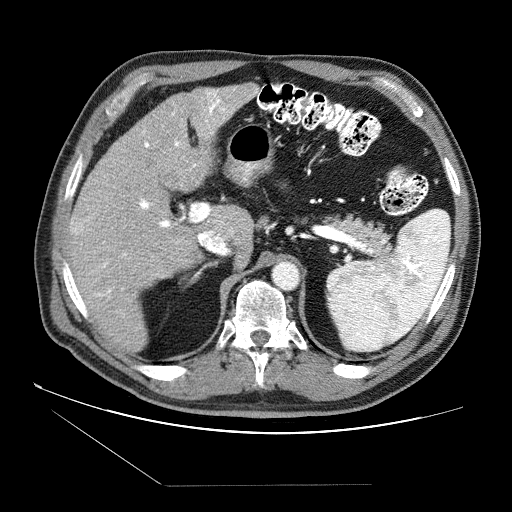
Contrast-enhanced abdominal CT (liver protocol), one axial slice; position 49 of 87 along the scan axis; reconstruction kernel STANDARD; 120 kVp; soft-tissue window (W 400 / L 40 HU); 2.5 mm slice thickness; 512 × 512 image matrix, field of view 400 × 400 mm. From the clinical record (not read from this slice): diagnosis: hepatocellular carcinoma (patient treated with transarterial chemoembolisation; whether this scan precedes or follows treatment is not stated here); TNM stage (as recorded): Stage-II; Child-Pugh class: B; tumour differentiation: no biopsy; tumour nodularity: multinodular.
Annotated regions visible in this slice (semi-automatic segmentation, software-assisted and operator-edited):
- liver parenchyma outside the tumour (the mass and vessels are separate outlines, so this box may not span the whole liver): box from (x=66, y=84) to (x=258, y=351) px
- mass: (x=69, y=217)–(x=86, y=234)
- liver vessels: (x=86, y=88)–(x=256, y=297)